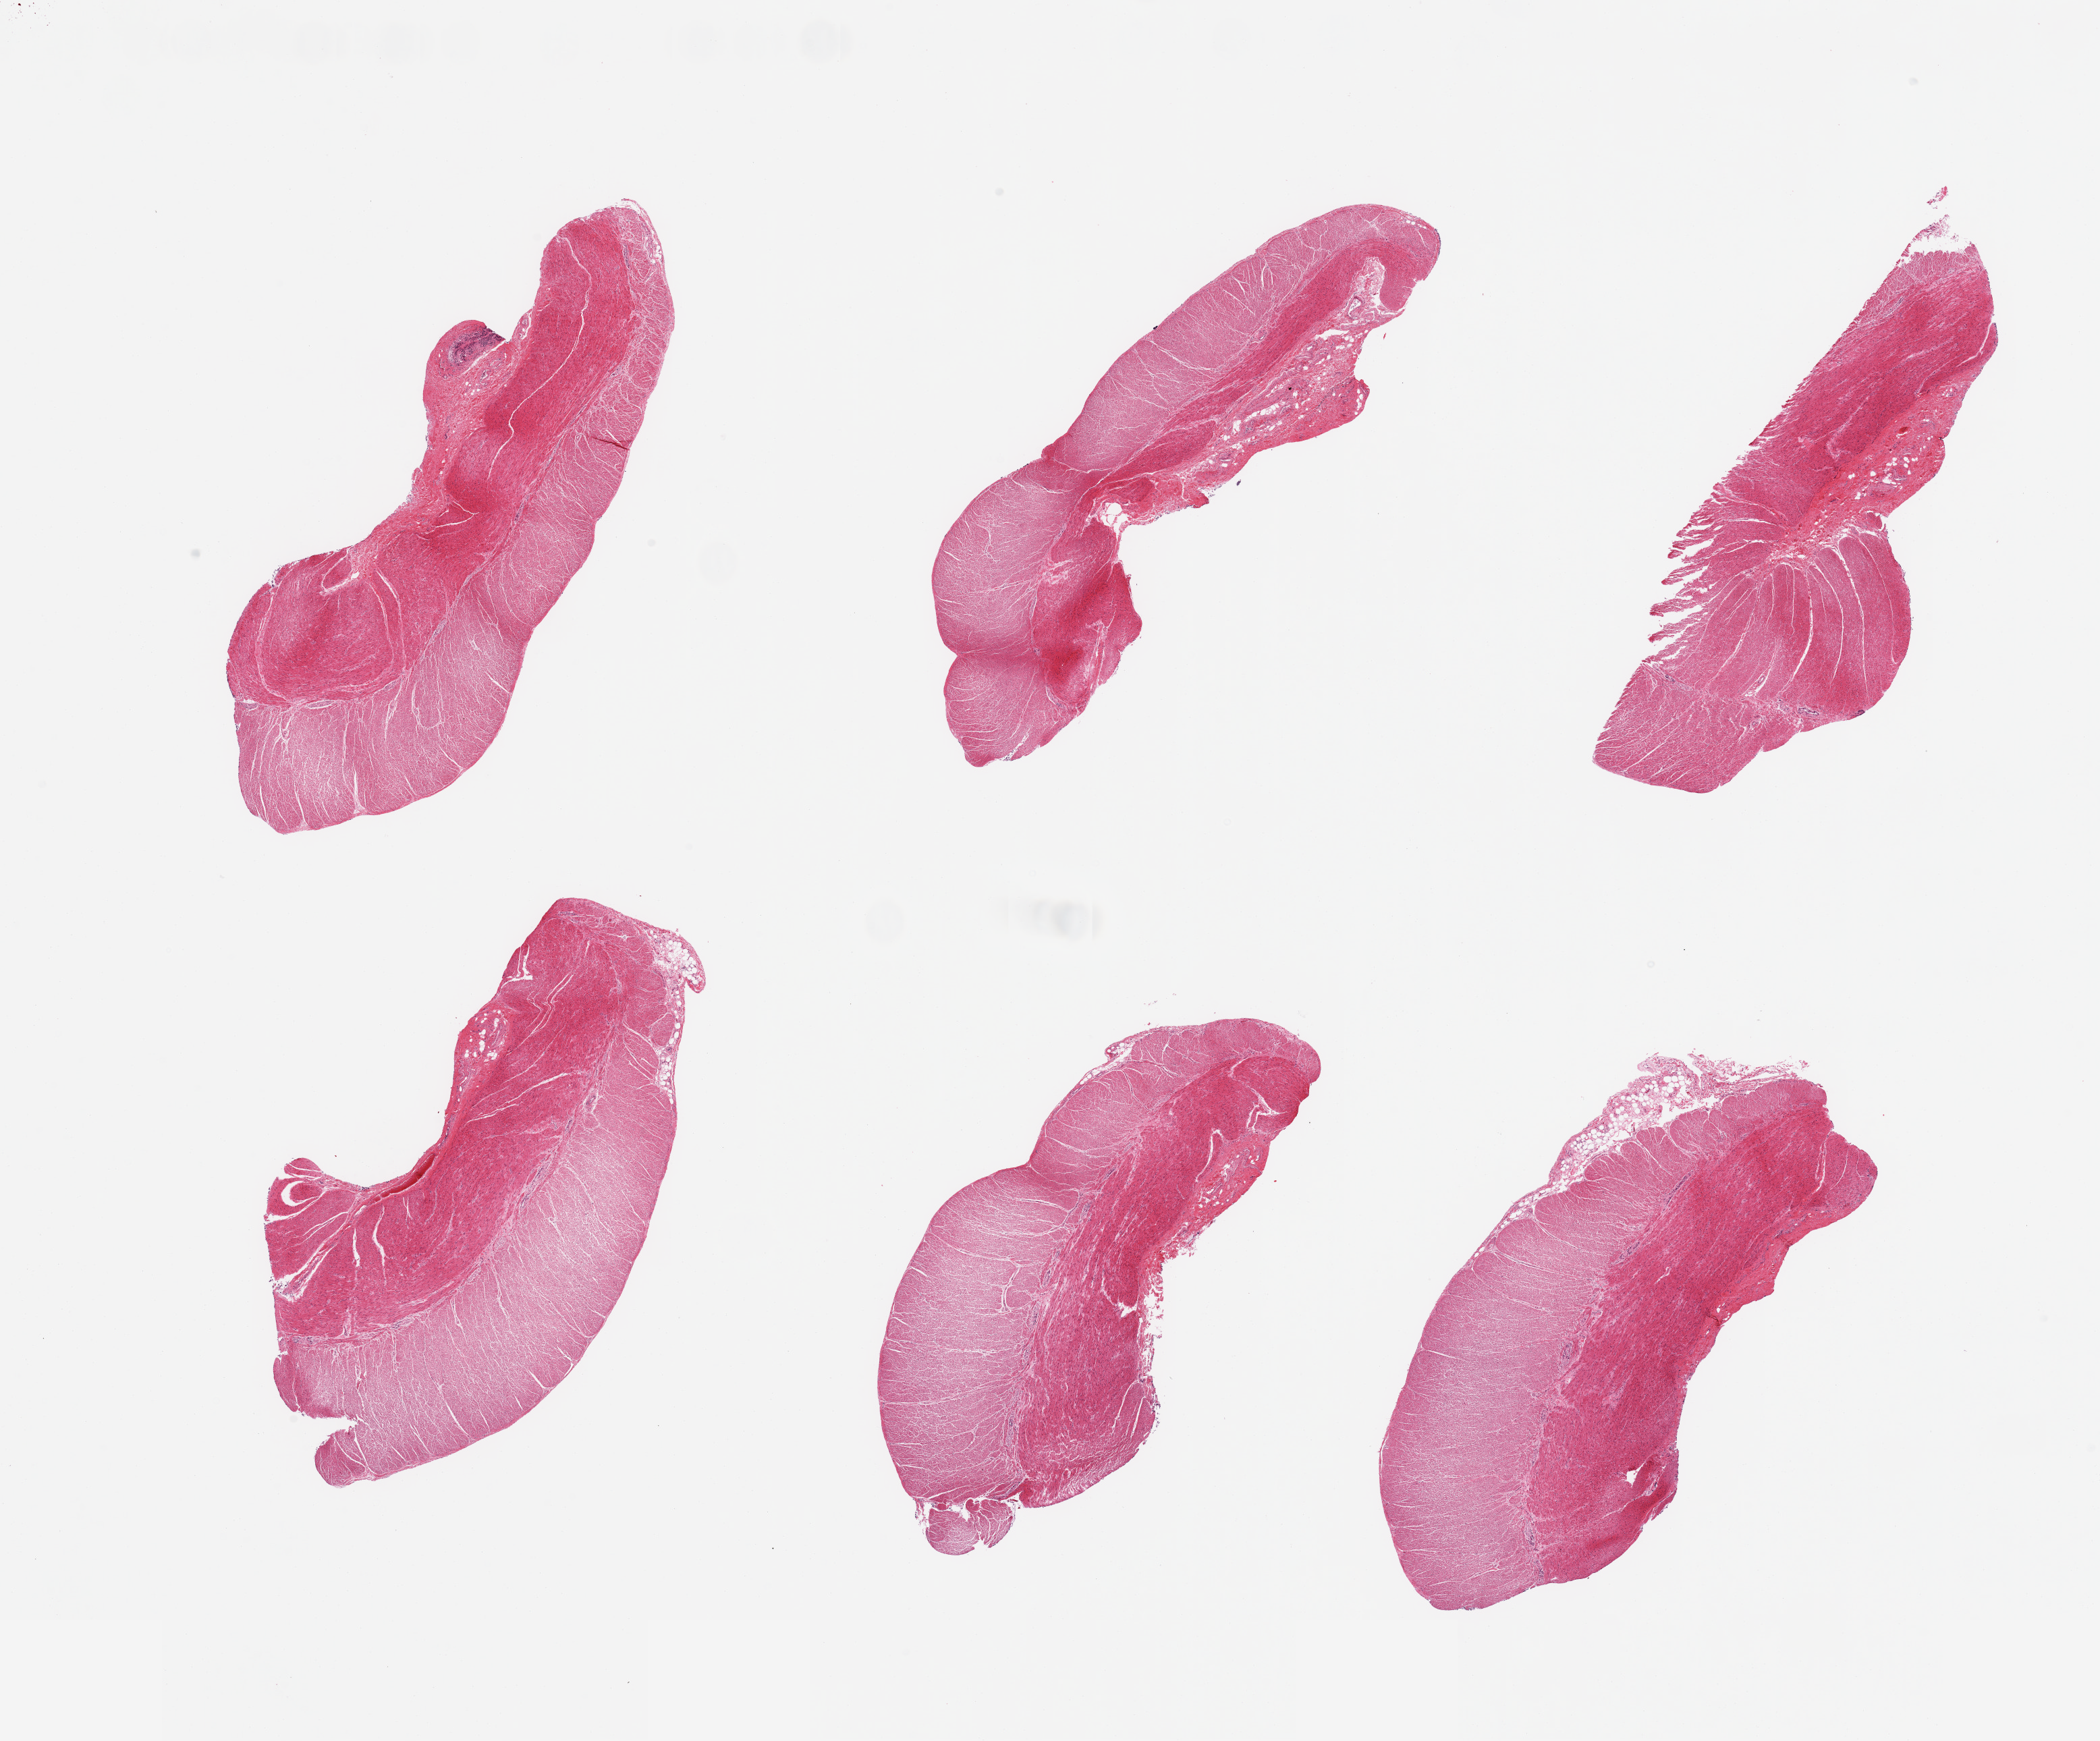
Whole-slide image, H&E stain — shown as a low-resolution overview of the whole scanned area (about 24.6 x 20.4 mm, acquisition: 20x scan). PAXgene-fixed paraffin-embedded (PFPE) section. Section of sigmoid colon (target tissue). Tissue donor sample.
Review note (as recorded): 6 pieces; well dissected.